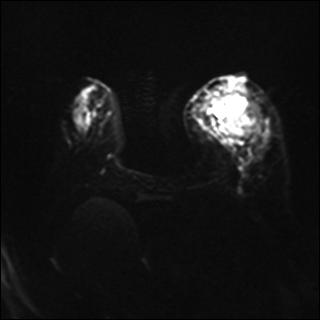
Breast MRI, one axial slice; slice 9 of 37 in the series (ordered by position); diffusion-weighted series; image 2 of 4 stored at this slice position (different b-values; order by instance number); 1.5 T; 4 mm slice thickness; 320 × 320 image matrix, field of view 320 × 320 mm. Female patient.
Outlined on this slice (expert manual segmentation):
- tumour on diffusion-weighted imaging: box from (x=215, y=93) to (x=259, y=140) px